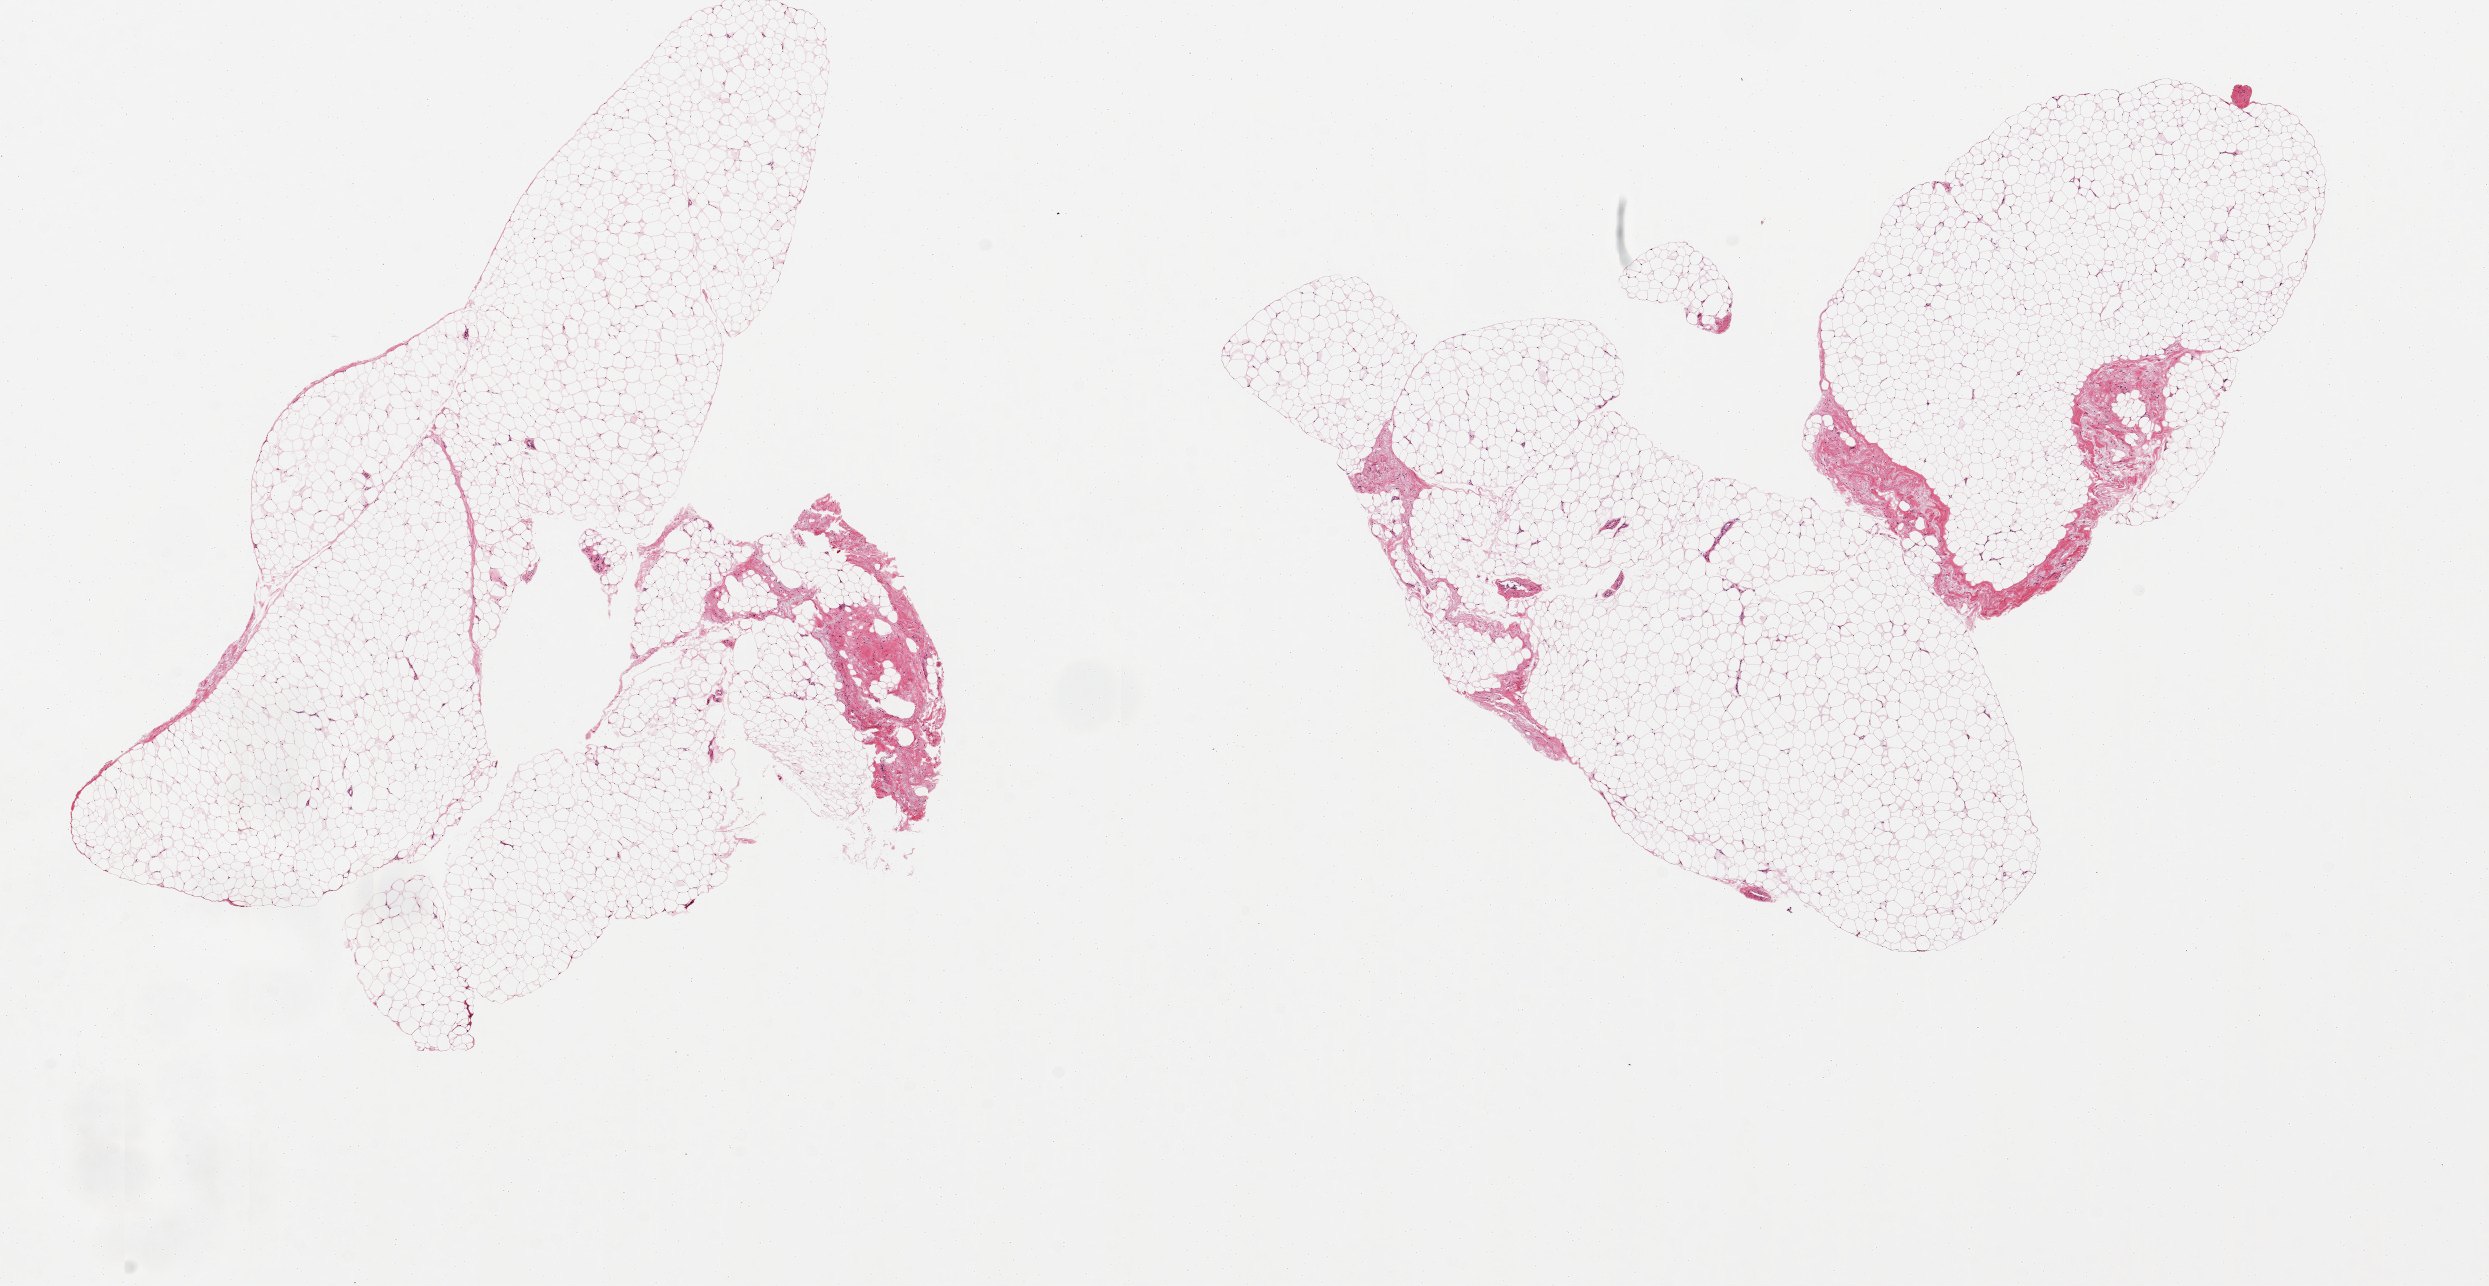
Whole-slide image, haematoxylin and eosin stain — whole scanned area (about 19.7 x 10.2 mm) shown as a low-resolution overview. PAXgene-fixed, paraffin-embedded tissue. Target tissue: adipose tissue. Tissue donor sample. Male donor.
Reviewer comment on this tissue sample: 2 aliquots, ~8x6mm.